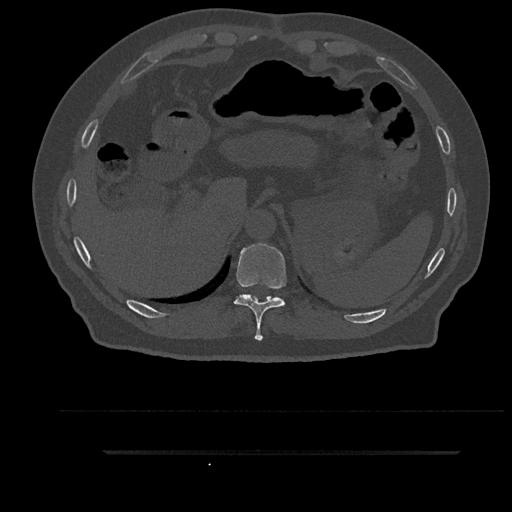
CT including the spine, one axial slice; position 356 of 797 along the scan axis; reconstruction kernel Br40s/3; 120 kVp; bone window (W 1800 / L 400 HU); 0.5 mm slice thickness; 512 × 512 image matrix. Male patient, age 63 years. Case-level facts recorded for this patient, not image findings: primary cancer: renal; vertebrae with lytic lesions (as recorded): T8.
Outlined on this slice (semi-automatically segmented with operator editing):
- T10 vertebra: bounding box <234,244,287,341> (left, top, right, bottom; pixels)
- T11 vertebra: <244,294,278,298>